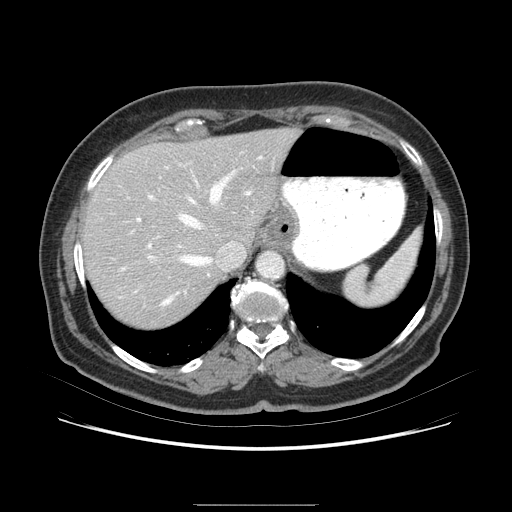
Contrast-enhanced abdominal CT (liver protocol), one axial slice. Slice 61 of 79 in the series (ordered by position). Soft-tissue window (W 400 / L 40 HU). 512 × 512 image matrix, field of view 380 × 380 mm. From the clinical record (not read from this slice): diagnosis: hepatocellular carcinoma (patient treated with transarterial chemoembolisation; whether this scan precedes or follows treatment is not stated here); TNM stage (as recorded): Stage-I.
Annotated regions visible in this slice (semi-automatic segmentation, software-assisted and operator-edited):
- liver parenchyma outside the tumour (the mass and vessels are separate outlines, so this box may not span the whole liver): bounding box (x1, y1, x2, y2) in pixels: (84, 134, 300, 310)
- liver vessels: (120, 168, 292, 262)